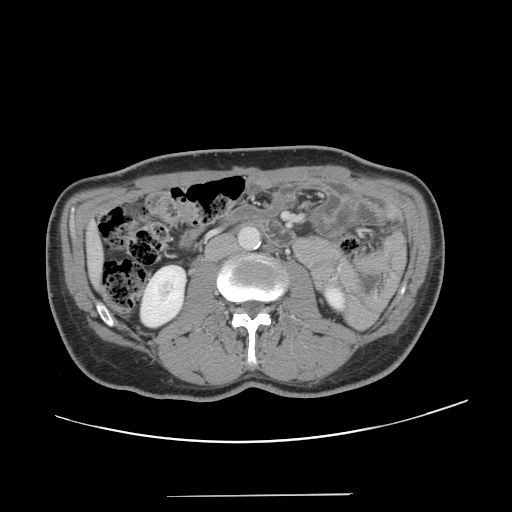
Contrast-enhanced abdominal CT, one axial slice; slice 40 of 131 in the series (ordered by position); 120 kVp; intravenous contrast given; soft-tissue window (W 400 / L 40 HU); 2.5 mm slice thickness; 512 × 512 image matrix, field of view 403 × 403 mm. Male patient, age 60 years. Case-level facts recorded for this patient, not image findings: diagnosis: colorectal cancer liver metastases, imaged before liver resection; multiple liver metastases: no; largest metastasis: 2.5 cm; chemotherapy before resection: no.
Annotated regions visible in this slice (expert manual segmentation):
- liver: box from (x=89, y=229) to (x=101, y=280) px
- planned liver remnant (the part of the liver to remain after resection): (x=89, y=228)–(x=101, y=281)